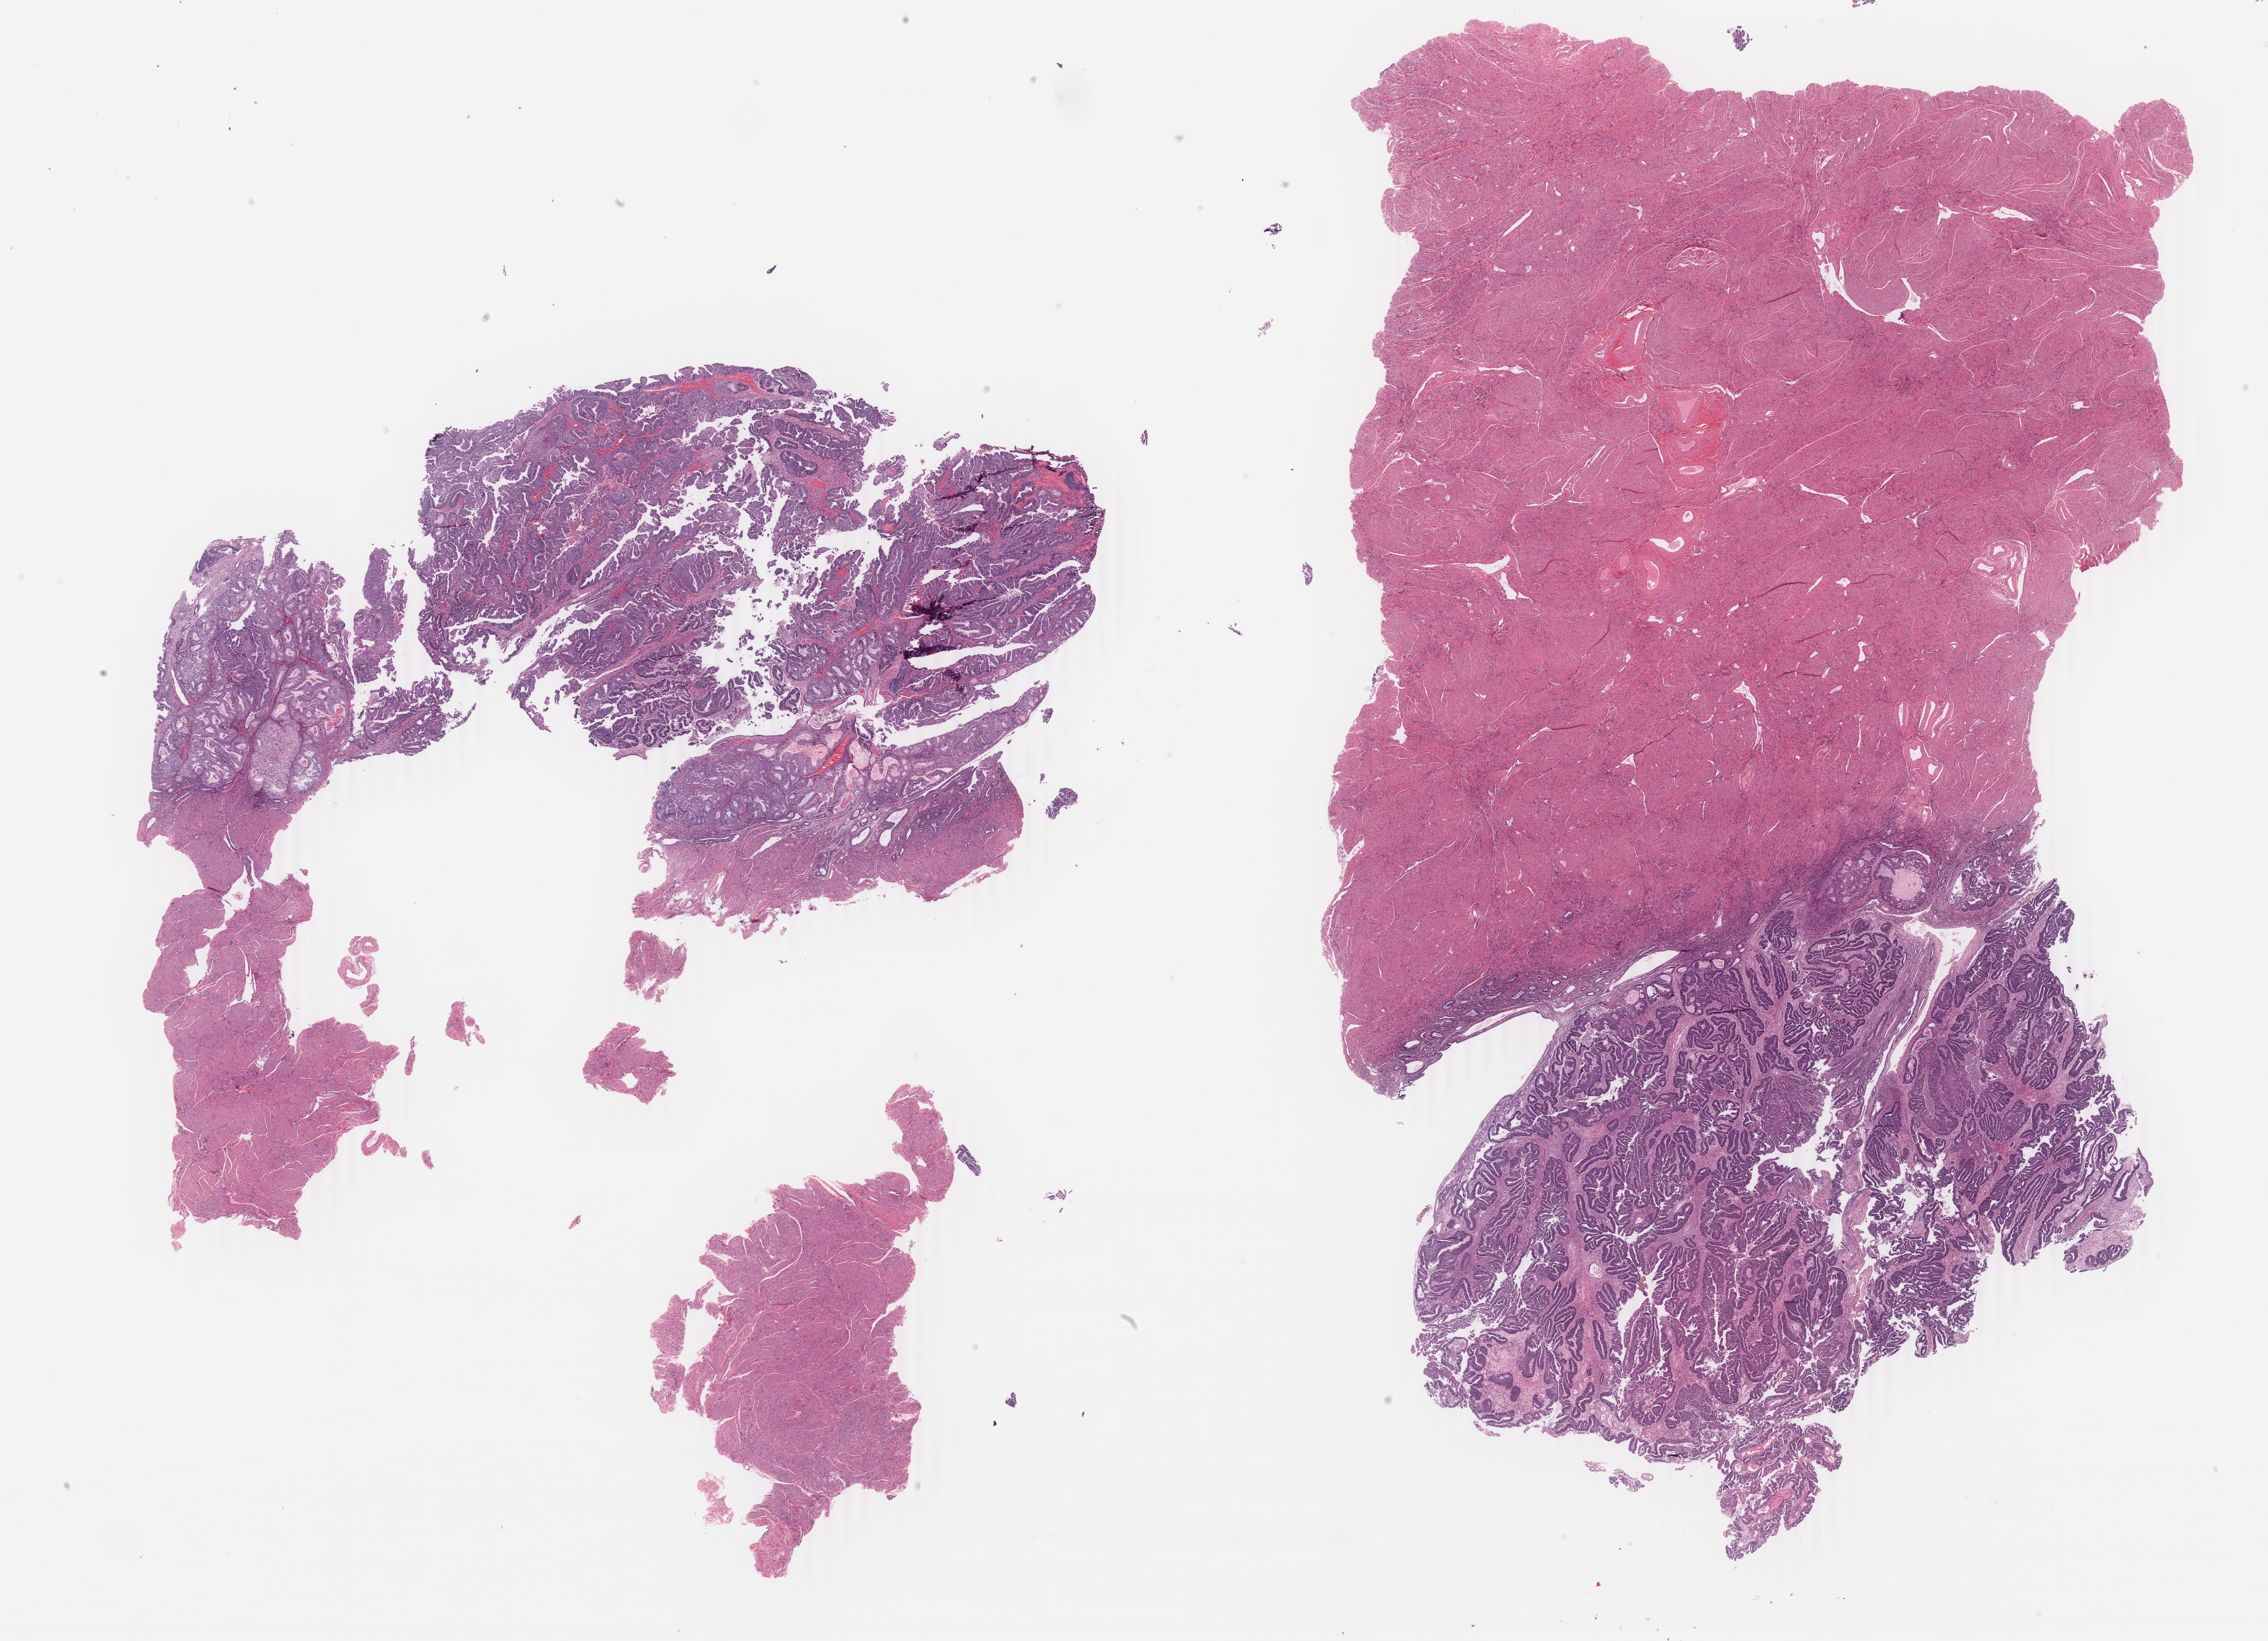
Digitized H&E tissue section (whole slide) — whole scanned area (about 29.5 x 21.3 mm, acquisition: 40x scan) shown as a low-resolution overview. Formalin-fixed paraffin-embedded (FFPE) diagnostic section. Sample: primary tumour, uterus. Patient: female, age at initial diagnosis 58 years. Histologic grade: G2 (moderately differentiated).
FIGO stage: IA. Lymph nodes positive (case pathology): 0 of 11 examined. Histologic diagnosis: Endometrioid adenocarcinoma, NOS (endometrium).